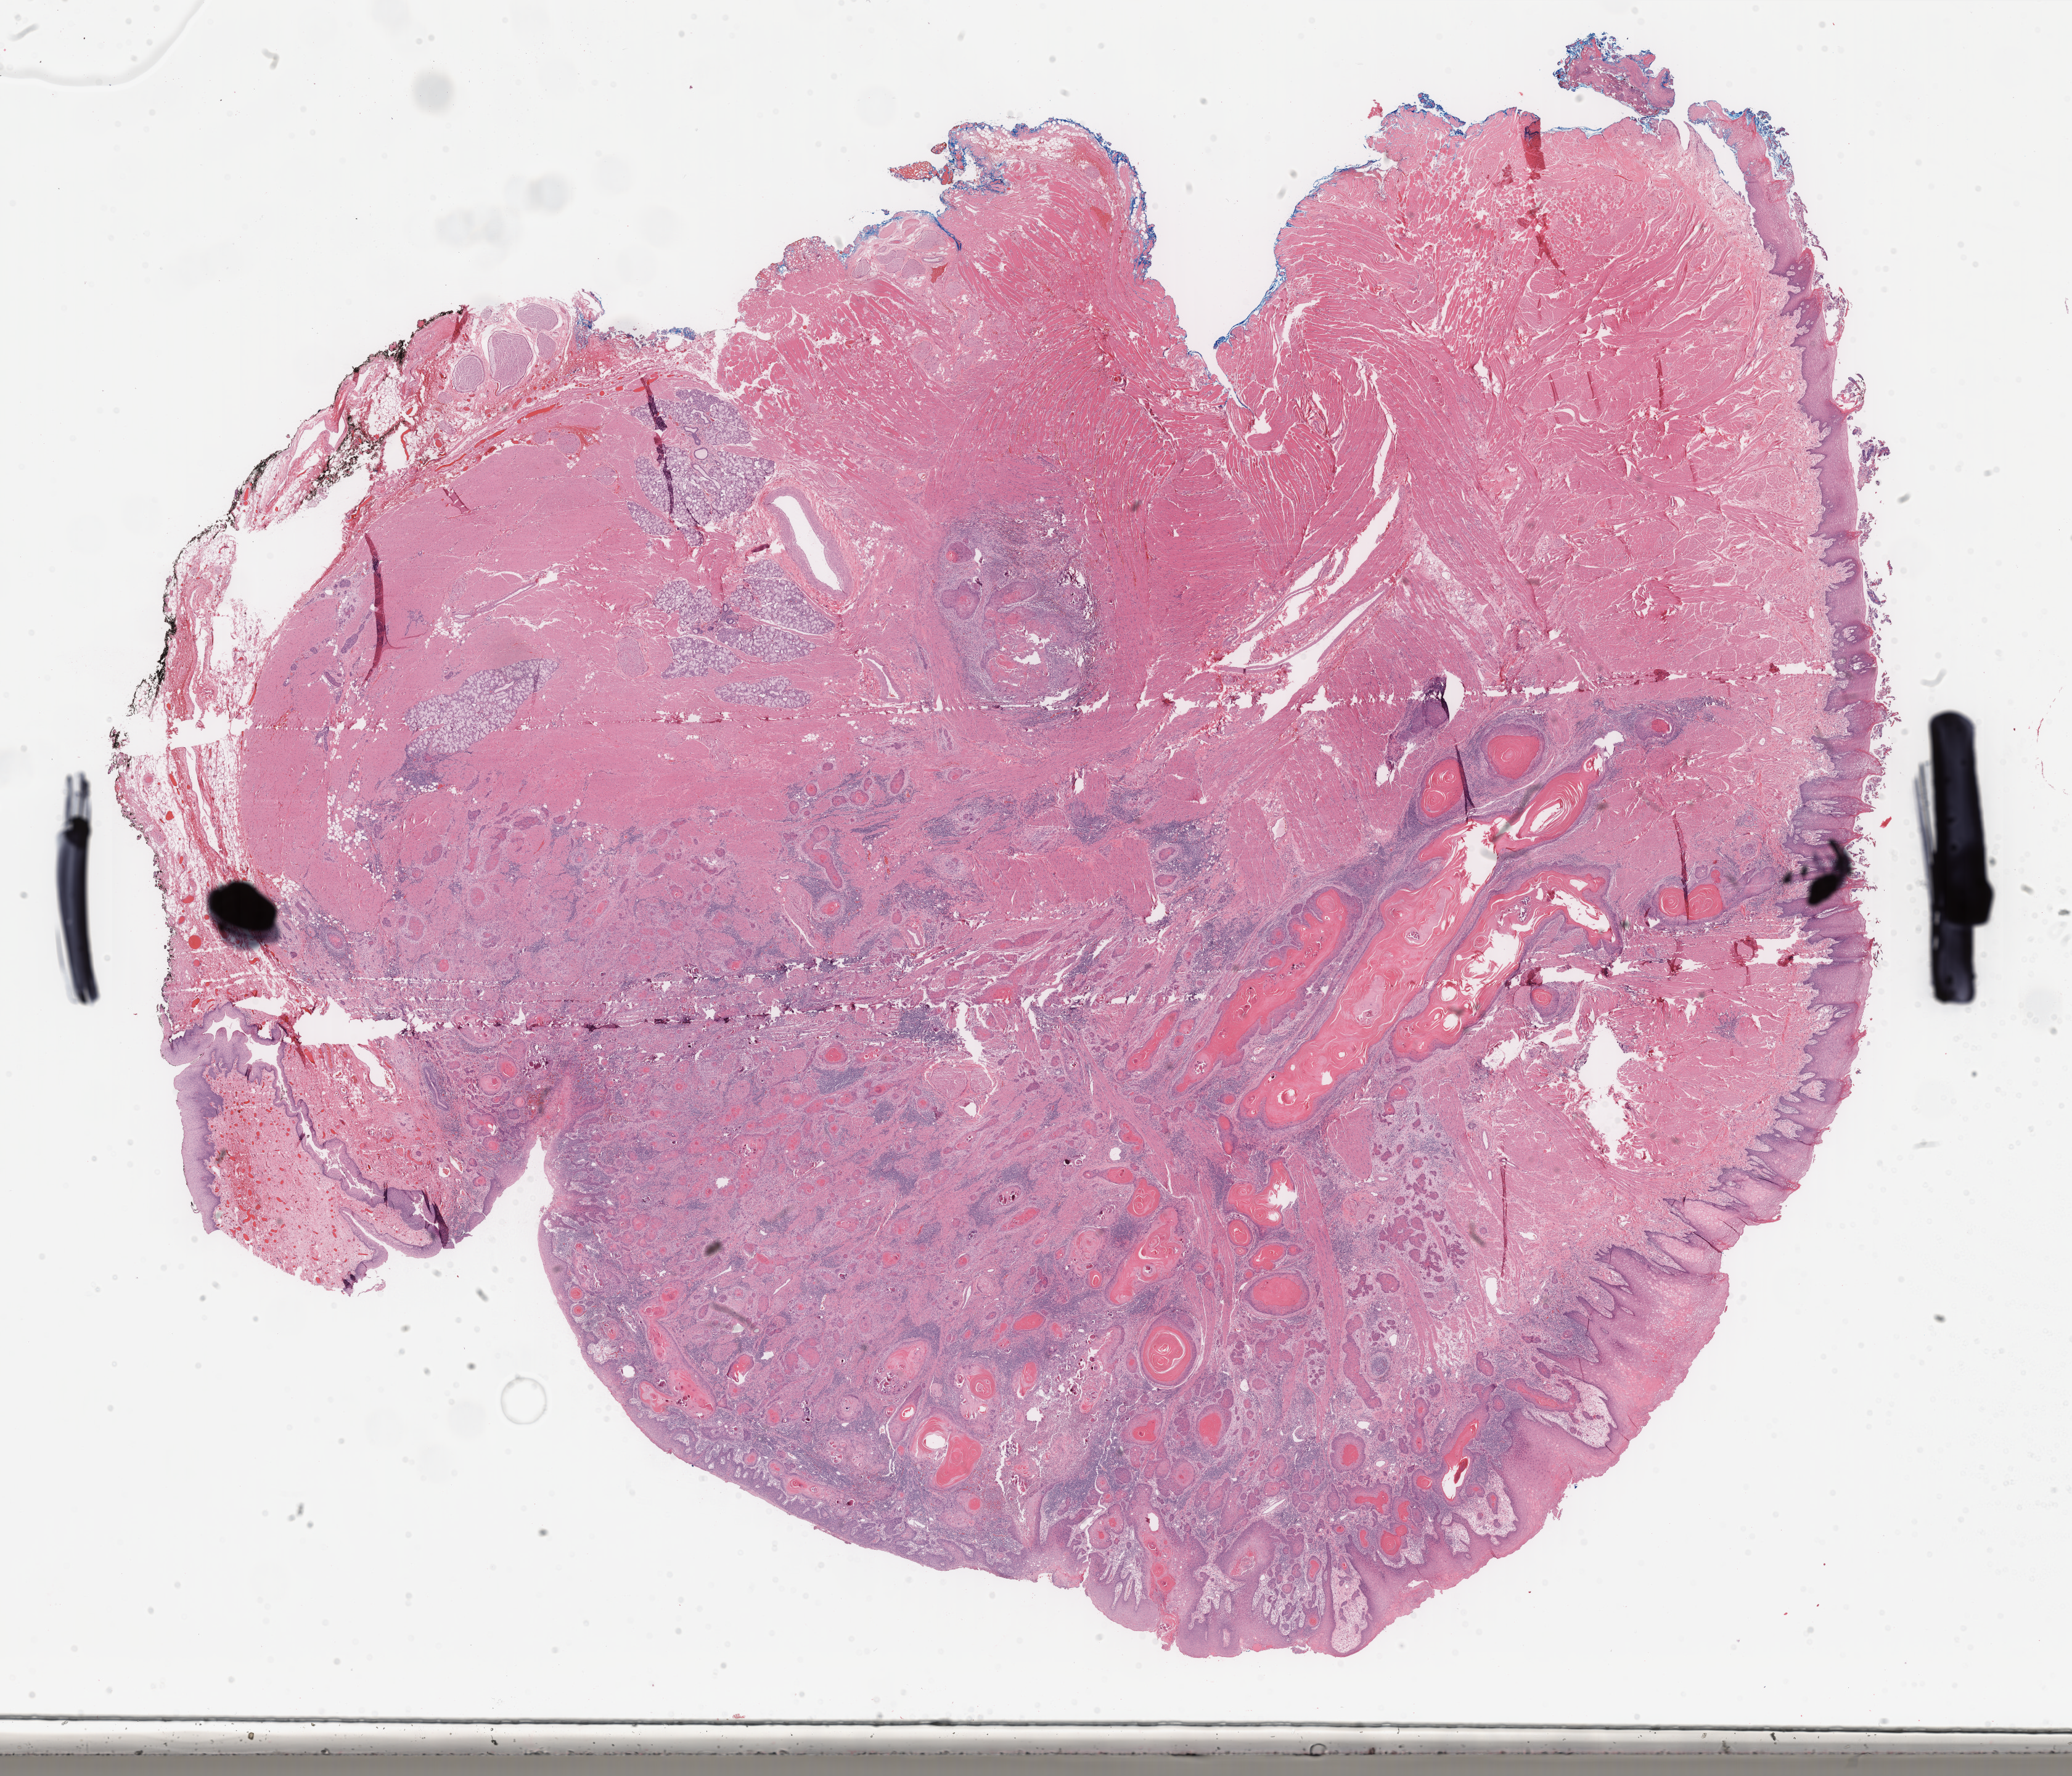
Whole-slide histology image, H&E-stained — low-resolution overview of the scanned area, about 26.6 x 22.8 mm (slide scanned at 40x). FFPE section. Sample: primary tumour, head and neck. Patient: female, age at initial diagnosis 24 years. Histologic grade: G1 (well differentiated).
* AJCC pathologic stage: I (7th edition)
* histologic diagnosis: Squamous cell carcinoma, keratinizing, NOS (tongue, NOS)